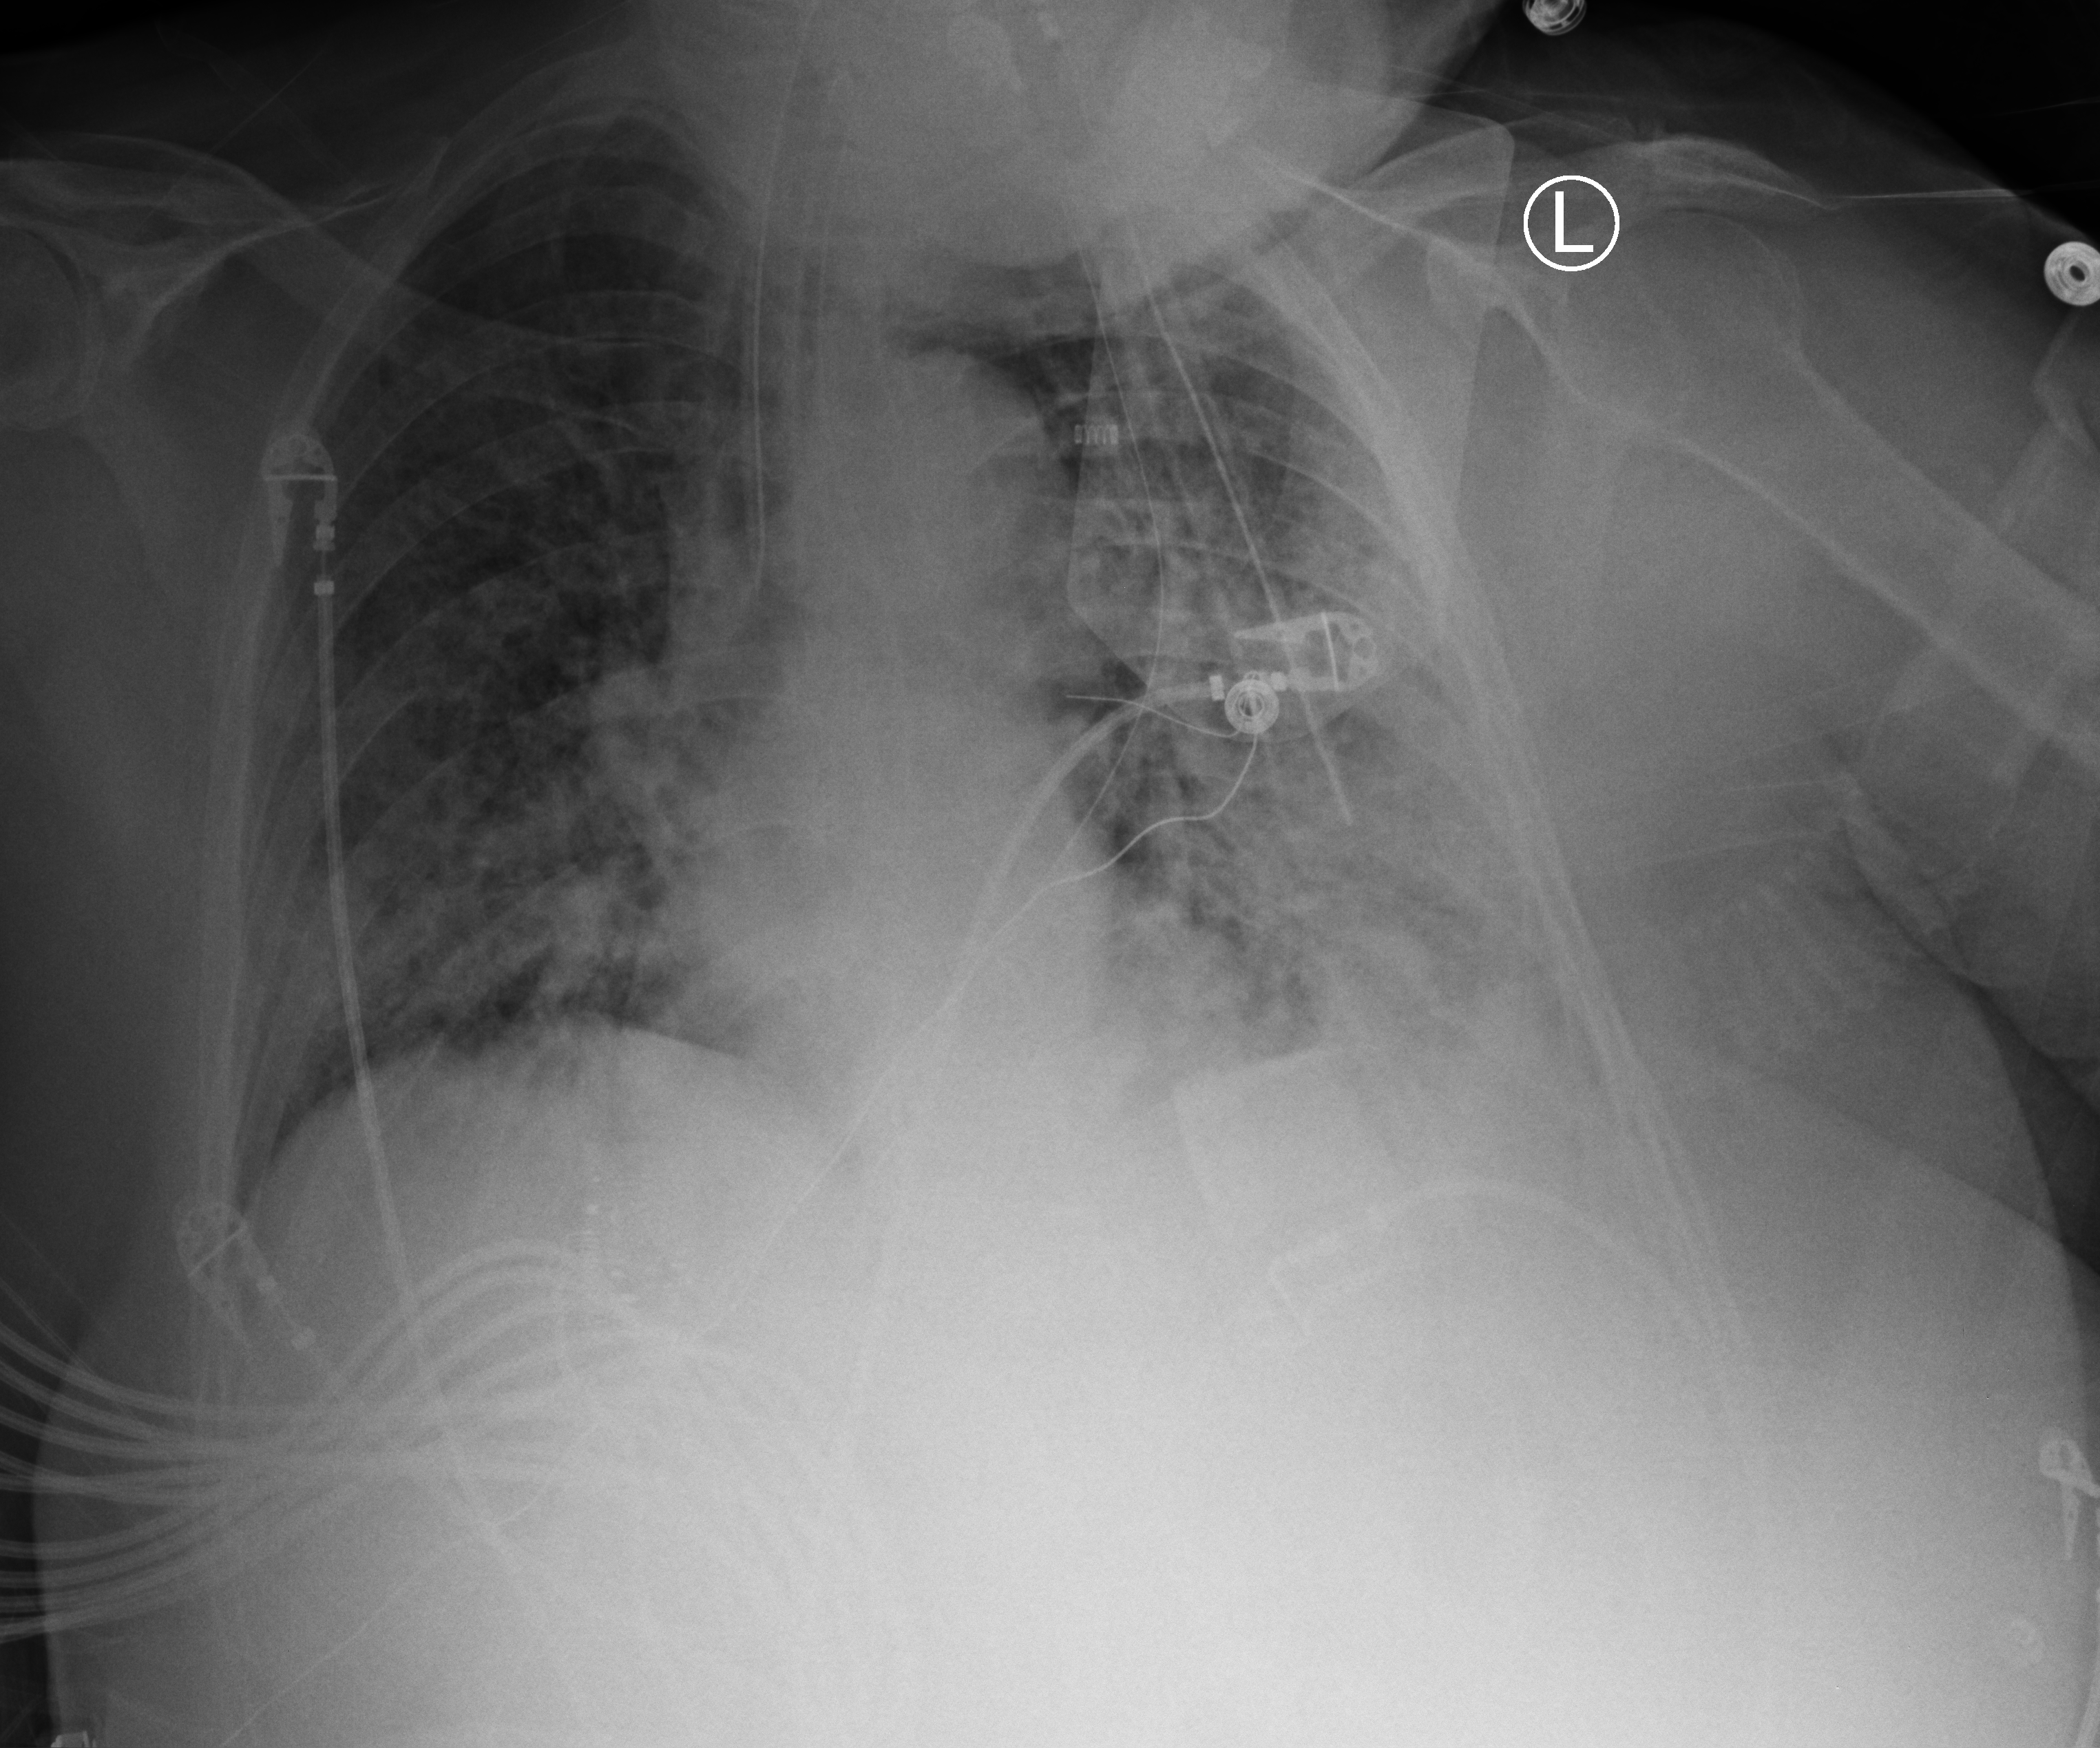
Chest X-ray (portable); anteroposterior (AP) projection. Female patient hospitalised with COVID-19, age 60–74 years.
Hospital-stay facts (about this admission, not read from this image; timing relative to this image not recorded): mechanically ventilated during this hospital stay: yes; length of hospital stay: 19 days.